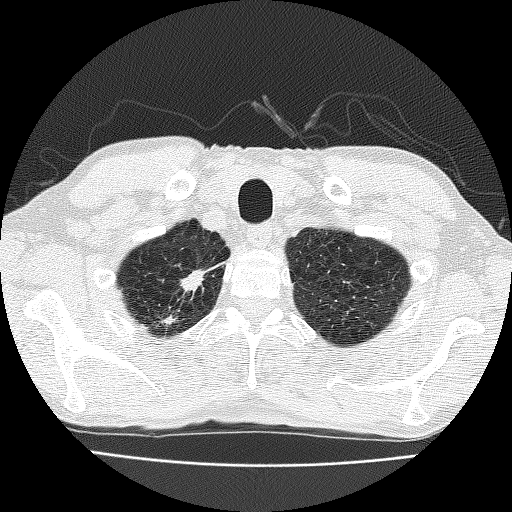
Low-dose screening chest CT, one axial slice. Position 159 of 185 along the scan axis. Reconstruction kernel FC51. Lung window (W 1500 / L -600 HU). 2 mm slice thickness. 512 × 512 image matrix, field of view 322 × 322 mm.
Structures marked on this image (outlined manually by an expert reader):
- lesion 1 (nodule, upper lobe of right lung): bounding box (x1, y1, x2, y2) in pixels: (180, 269, 205, 292)
- lesion 2 (nodule, upper lobe of right lung): (163, 317, 173, 324)